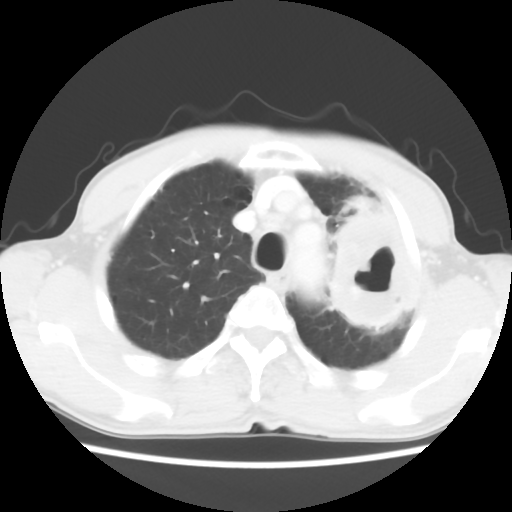
Chest CT, one axial slice; slice 47 of 60 in the series (ordered by position); 120 kVp; lung window (W 1500 / L -600 HU); 5 mm slice thickness; 512 × 512 image matrix, field of view 308 × 308 mm. Male patient, age 64 years. From the clinical record (not read from this slice): clinical TNM (as recorded): T3 N3 M0.
Structures marked on this image (rectangle marked by the reading radiologist):
- lung tumour (recorded histology: adenocarcinoma): box from (x=318, y=186) to (x=431, y=346) px